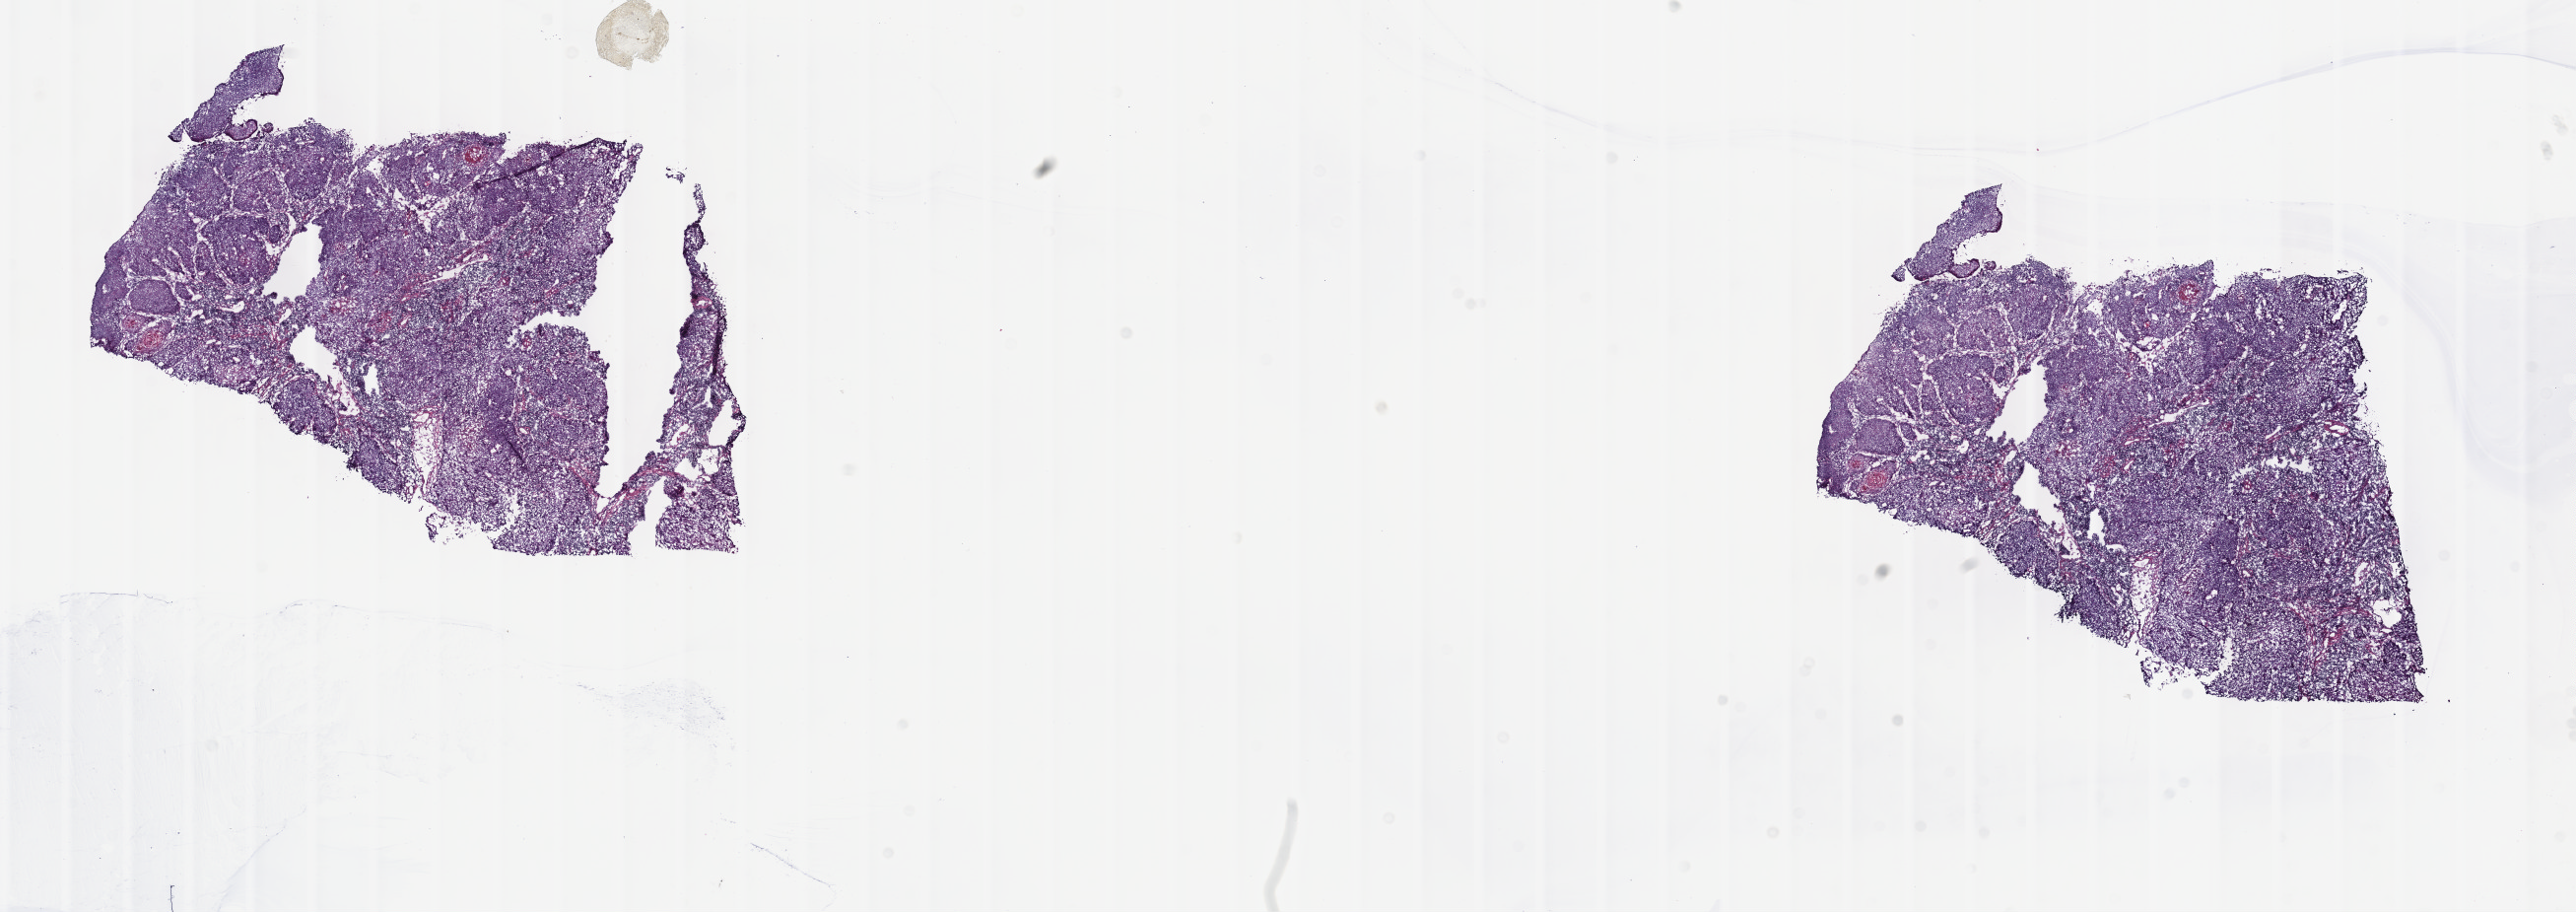
H&E whole-slide image, whole scanned area (about 21.1 x 7.5 mm, slide scanned at 40x) shown as a low-resolution overview. Frozen section. Sample: primary tumour, cervix. Female, age 69 years at initial diagnosis. Histologic grade: G3 (poorly differentiated). Pathologist review of this section (percent, as recorded): tumour cells 85%, tumour nuclei 85%, normal cells 0%, stromal cells 15%, necrosis 0%. Inflammatory infiltration, as recorded: lymphocyte infiltration 10%, monocyte infiltration 0%, neutrophil infiltration 0%.
- lymph nodes positive (case pathology): 0 of 10 examined
- diagnosis: Squamous cell carcinoma, NOS (cervix uteri)
- FIGO stage: IB2